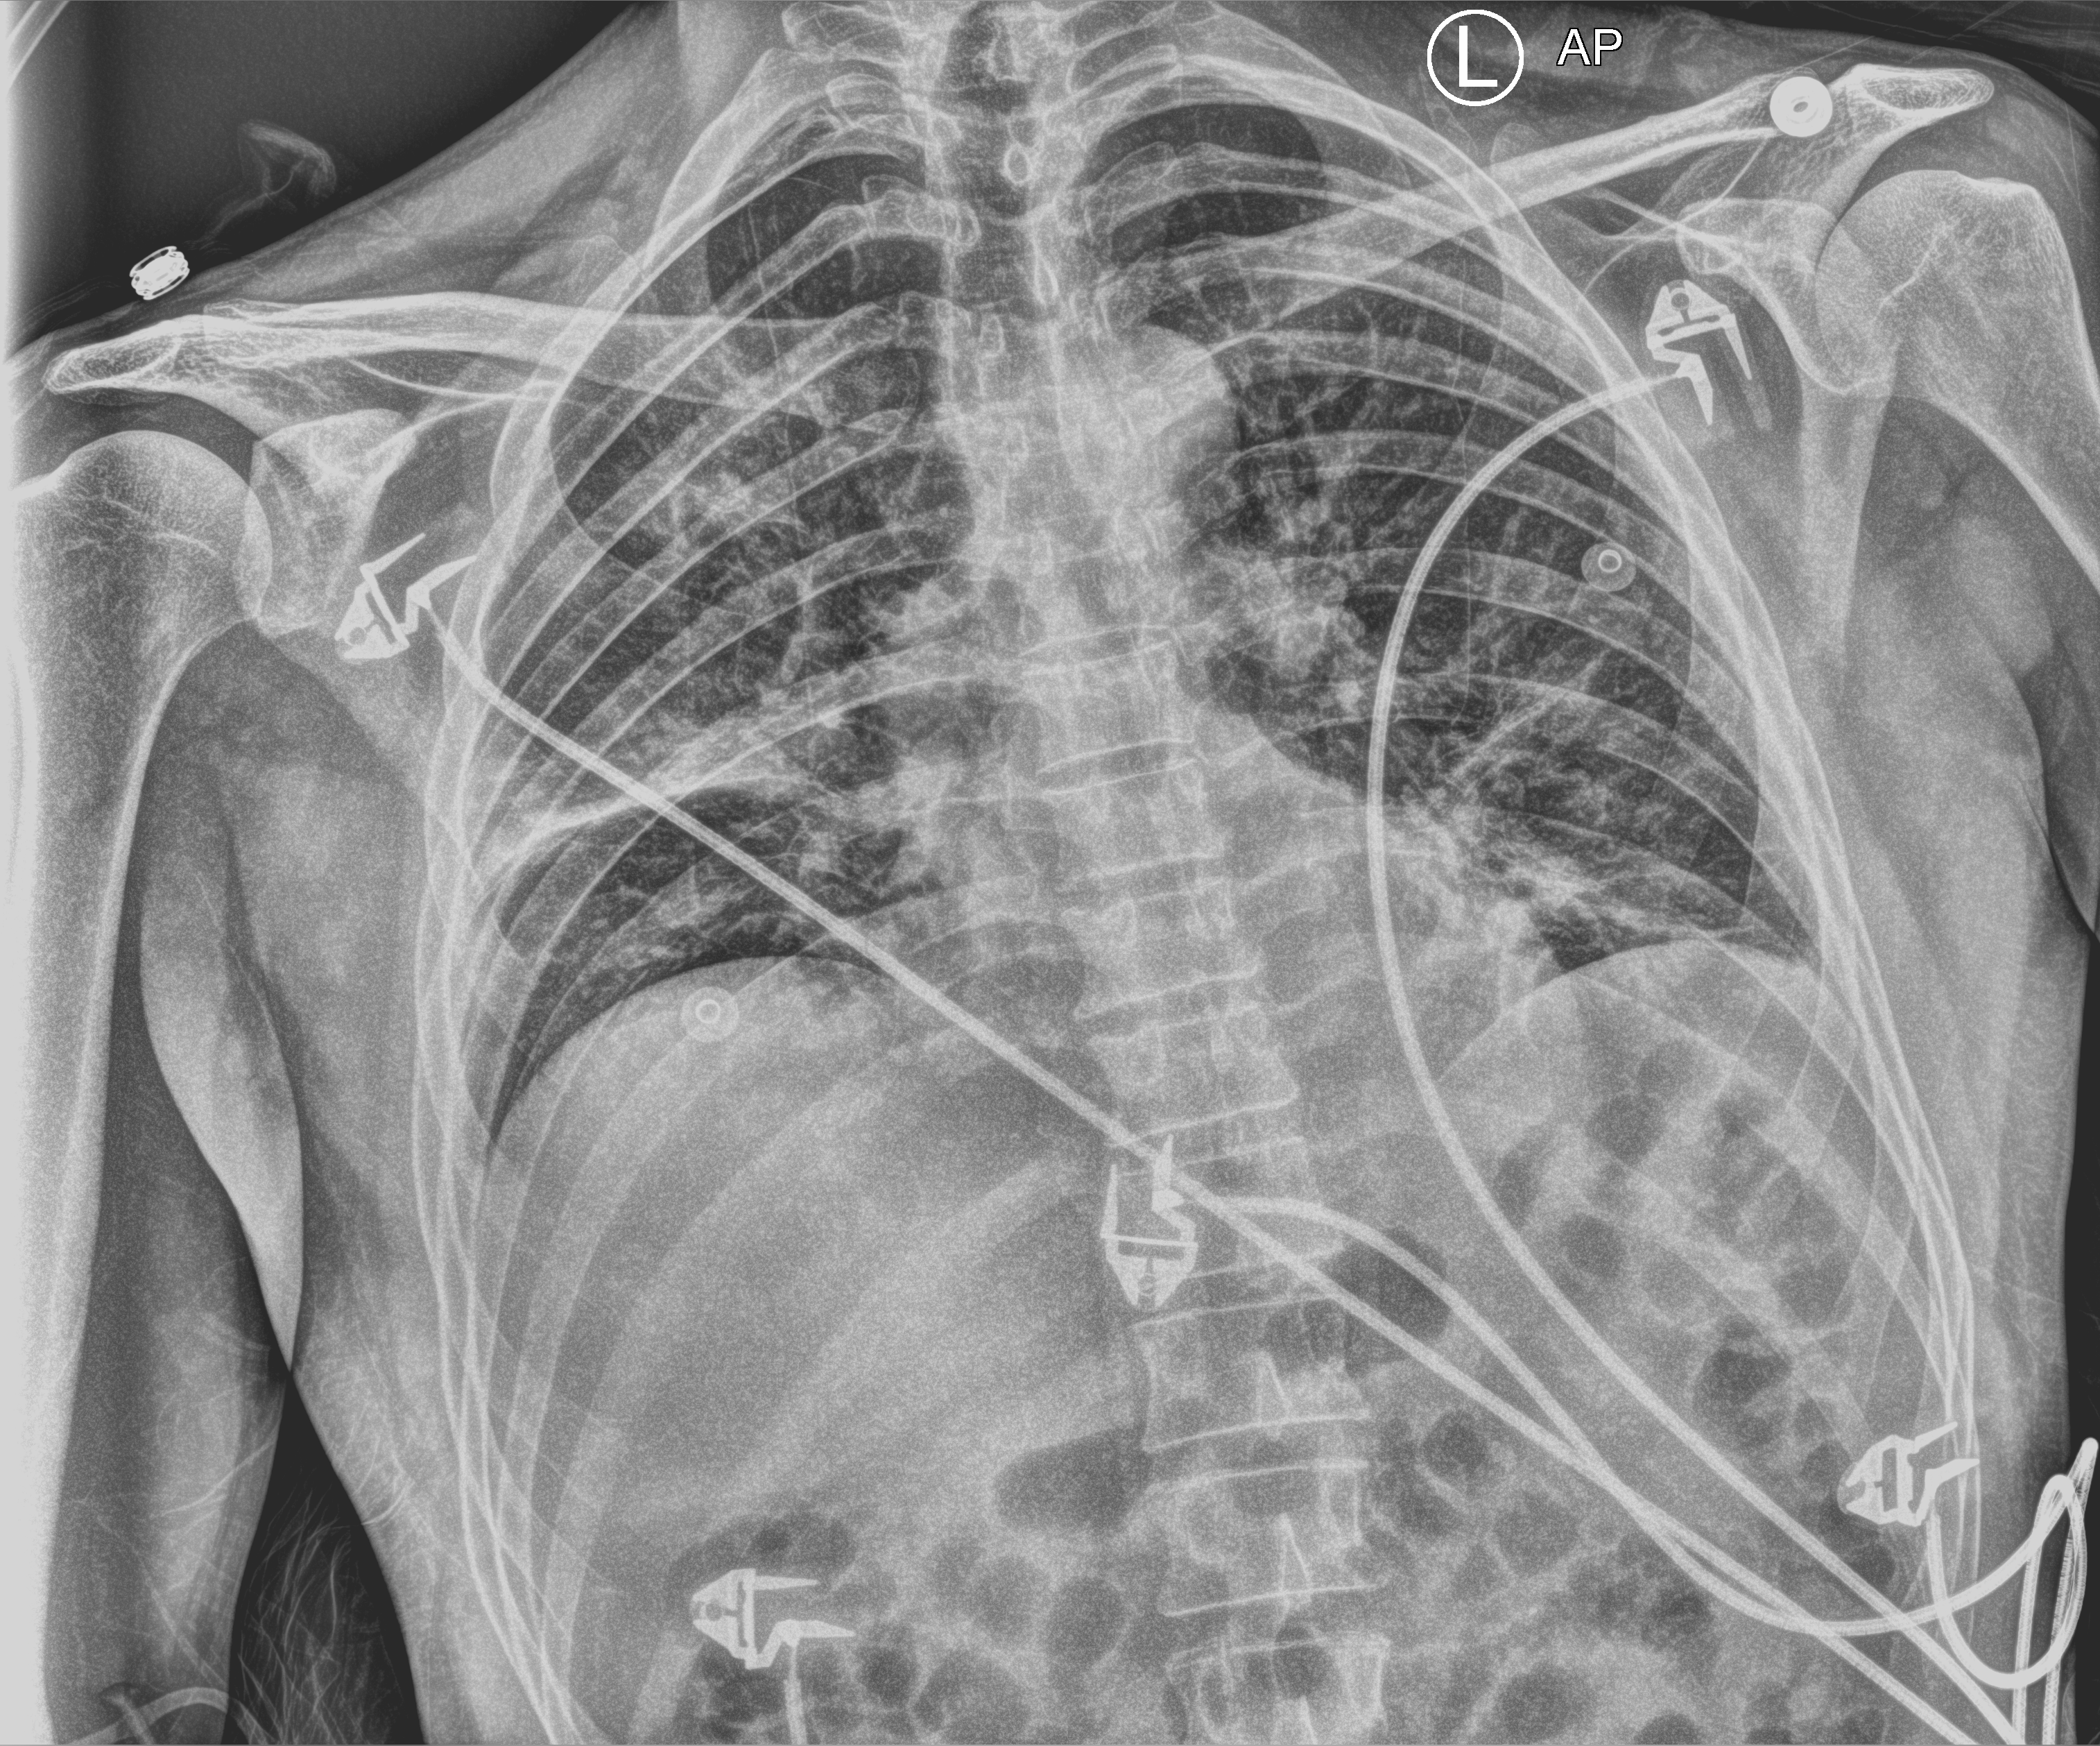
Chest X-ray (portable); anteroposterior (AP) projection. Patient hospitalised with COVID-19; male, aged 18–59 years.
Admission-level facts for this patient (not findings on this image; timing relative to this image not recorded):
- mechanically ventilated during this hospital stay: no
- hypertension (admission record): no
- admitted to intensive care during this hospital stay: no